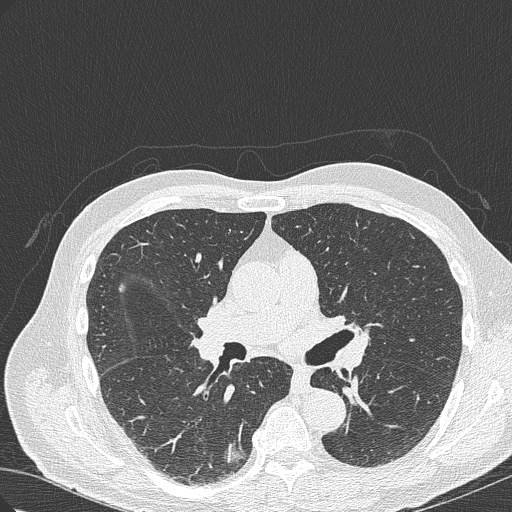
Chest CT (low-dose screening protocol), one axial image; baseline screening round; lung window (W 1500 / L -600 HU); 1 mm slice thickness; lung (sharp) reconstruction kernel (B50f); slice 138 of 322 in the series. Male, age 70 years at enrolment. Current smoker at enrolment.
Lesion marked by an expert reader, bounding box [x1, y1, x2, y2] px = [199, 419, 262, 476]. The screening reader recorded 4 non-calcified nodules or masses ≥4 mm on this exam (right lower lobe, right lower lobe, right upper lobe, right lower lobe); which of them this box marks is not recorded. Official screen result: positive, change unspecified: nodule(s) >= 4 mm or enlarging nodule(s), mass(es), or other non-specific abnormalities suspicious for lung cancer.